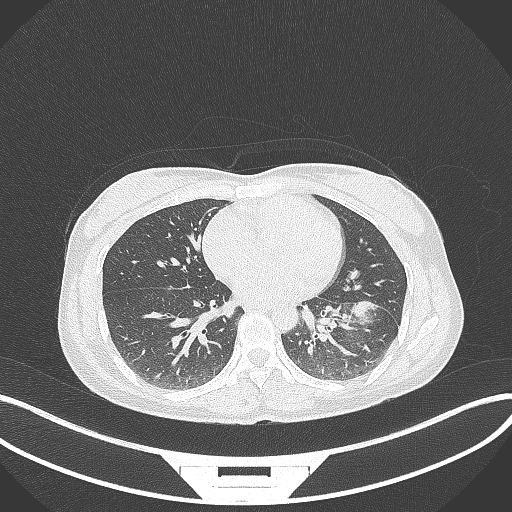
Chest CT, one axial slice. Slice 35 of 244 in the series (ordered by position). 120 kVp. Lung window (W 1500 / L -600 HU). 512 × 512 image matrix, field of view 400 × 400 mm. Patient: female, 41 years. From the clinical record (not read from this slice): clinical TNM (as recorded): T2a N3 M1b.
Structures marked on this image (rectangle marked by the reading radiologist):
- lung tumour (recorded histology: adenocarcinoma): bounding box (x1, y1, x2, y2) in pixels: (346, 296, 388, 331)